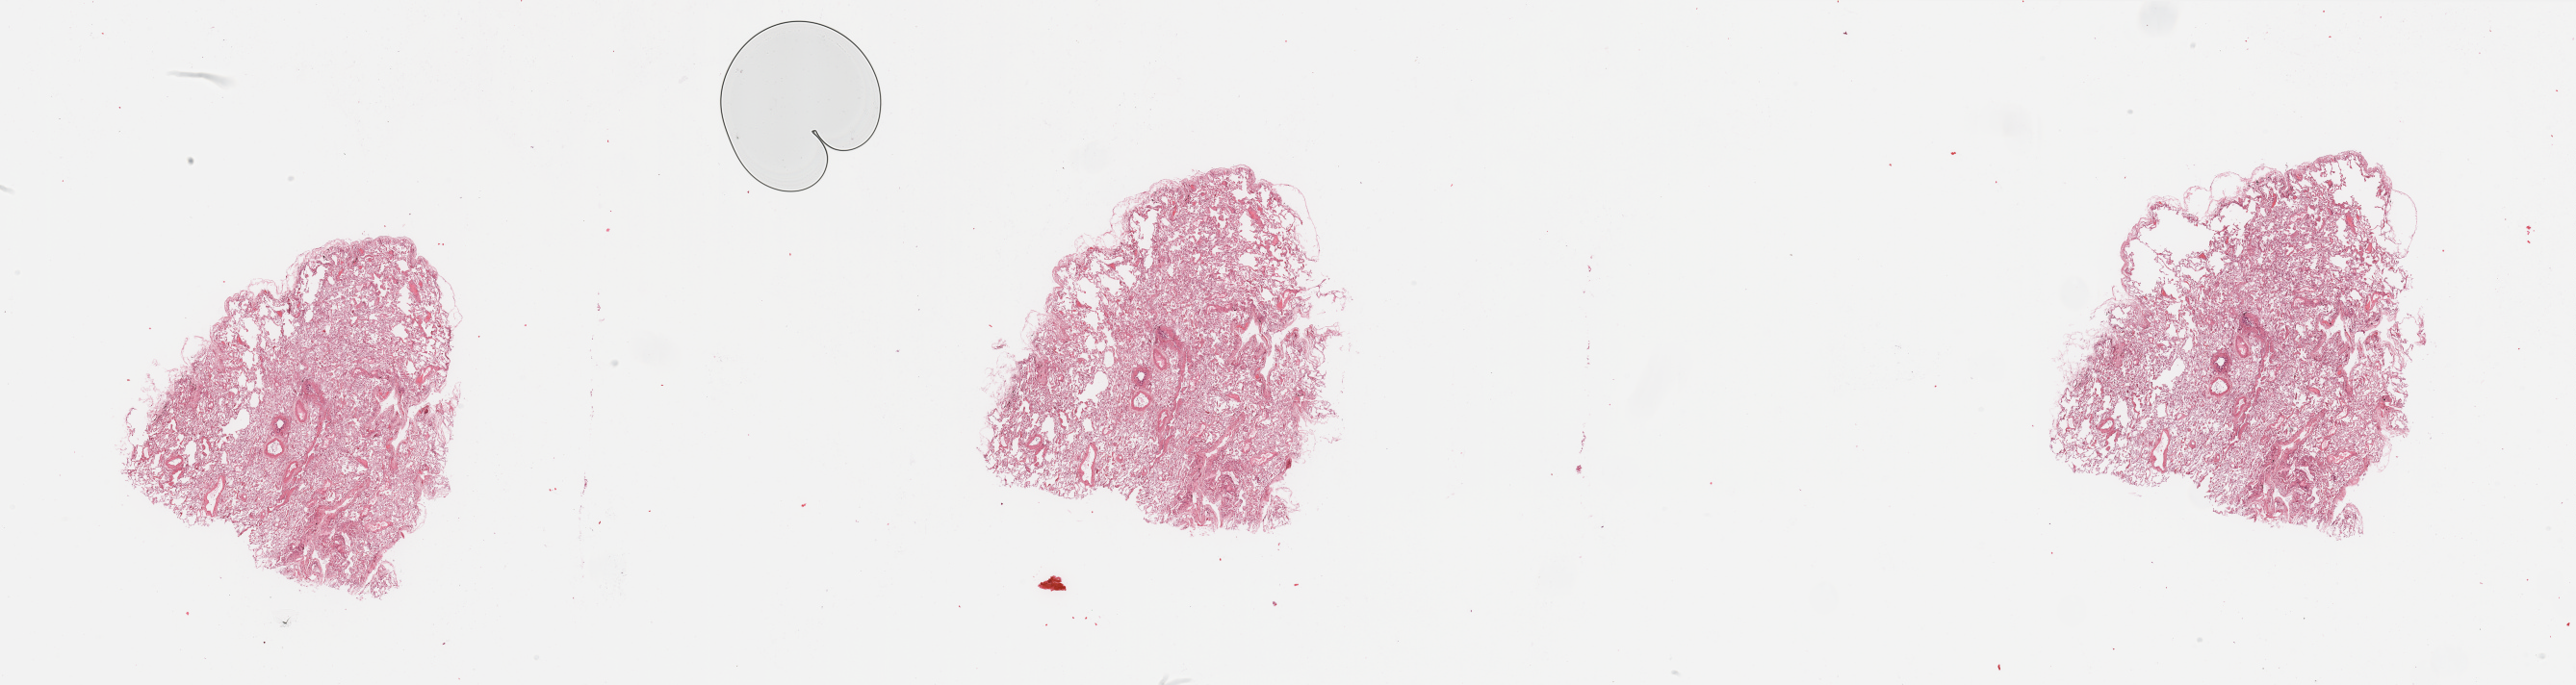
Whole-slide histology image, H&E-stained — shown as a low-resolution overview of the whole scanned area (about 42.3 x 11.3 mm); normal (non-tumour) tissue sample, sampled site: lung. 64-year-old female patient.
This section: normal (non-tumour) tissue from the same patient. Patient diagnosis: Squamous cell carcinoma, NOS.